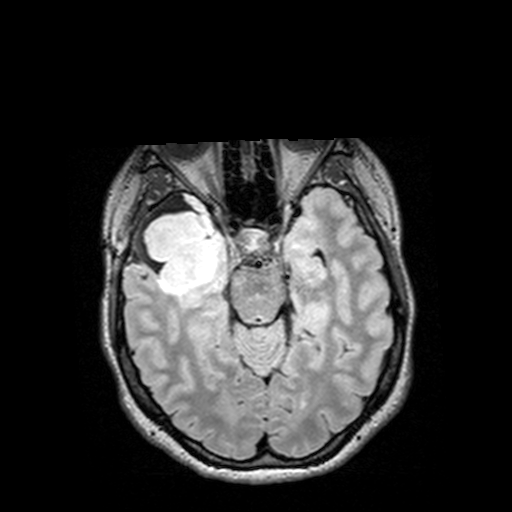
Brain MRI from a brain-tumour surgery series, one axial slice; slice 91 of 144 in the series (ordered by position); T2 FLAIR; 1 mm slice thickness; 512 × 512 image matrix. Case-level facts recorded for this patient, not image findings: histopathology: Astrocytoma; WHO grade: 3; IDH mutation: yes; tumour location: Right Insular Temporal.
Outlined on this slice (outlined manually by an expert reader):
- tumour: bounding box (x1, y1, x2, y2) in pixels: (126, 193, 232, 308)